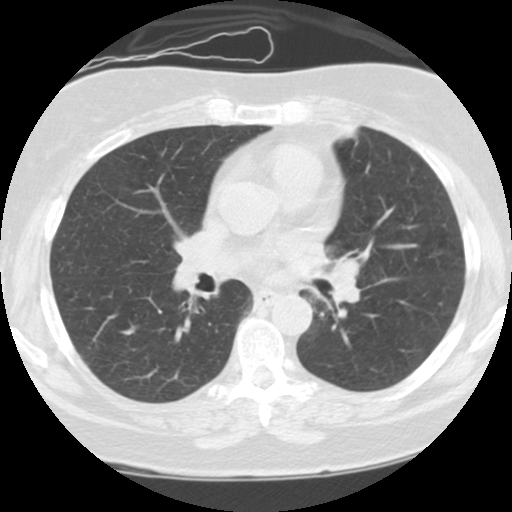
Low-dose screening chest CT, one axial slice; slice 60 of 108 in the series (ordered by position); reconstruction kernel STANDARD; lung window (W 1500 / L -600 HU); 2.5 mm slice thickness; 512 × 512 image matrix, field of view 300 × 300 mm.
Outlined on this slice (expert manual segmentation):
- lesion 1 (tumor, hilum of left lung): box from (x=331, y=256) to (x=362, y=305) px